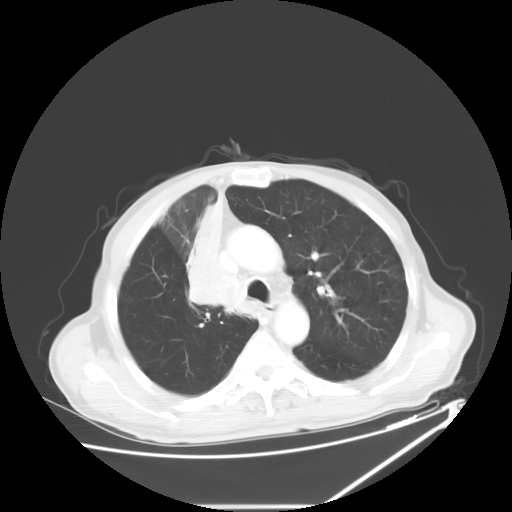
Chest CT, one axial slice; position 43 of 60 along the scan axis; reconstruction kernel STANDARD; 120 kVp; lung window (W 1500 / L -600 HU); 5 mm slice thickness; 512 × 512 image matrix, field of view 410 × 410 mm. Patient: male, 73 years. From the clinical record (not read from this slice): clinical TNM (as recorded): T2a N1 M0.
Outlined on this slice (rectangle marked by the reading radiologist):
- lung tumour (recorded histology: squamous cell carcinoma): box from (x=178, y=192) to (x=244, y=325) px